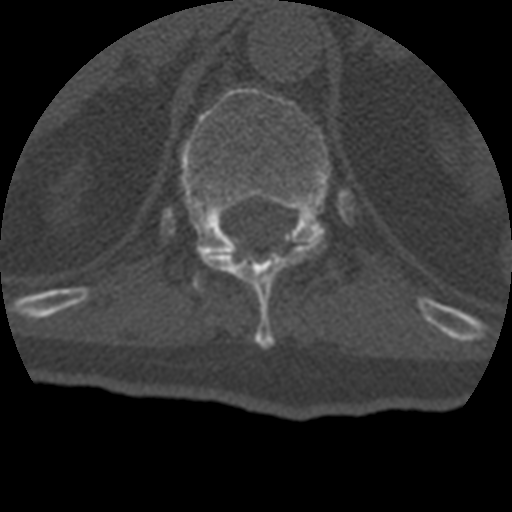
CT including the spine, one axial slice. Position 184 of 399 along the scan axis. 120 kVp. Bone window (W 1800 / L 400 HU). 512 × 512 image matrix. Patient age 69 years. Case-level facts recorded for this patient, not image findings: primary cancer: prostate.
Structures marked on this image (semi-automatic segmentation, software-assisted and operator-edited):
- T11 vertebra: bounding box <205,236,327,348> (left, top, right, bottom; pixels)
- T12 vertebra: <181,87,331,282>